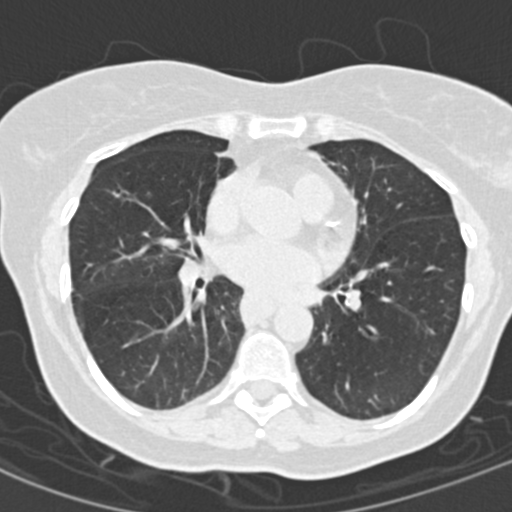
Low-dose screening chest CT, one axial slice; reconstruction kernel B30f; lung window (W 1500 / L -600 HU); 2 mm slice thickness; 512 × 512 image matrix.
Annotated regions visible in this slice (expert manual segmentation):
- lesion 1 (nodule, middle lobe of right lung): bounding box (x1, y1, x2, y2) in pixels: (146, 191, 152, 197)
- lesion 2 (nodule, middle lobe of right lung): (111, 185, 123, 199)